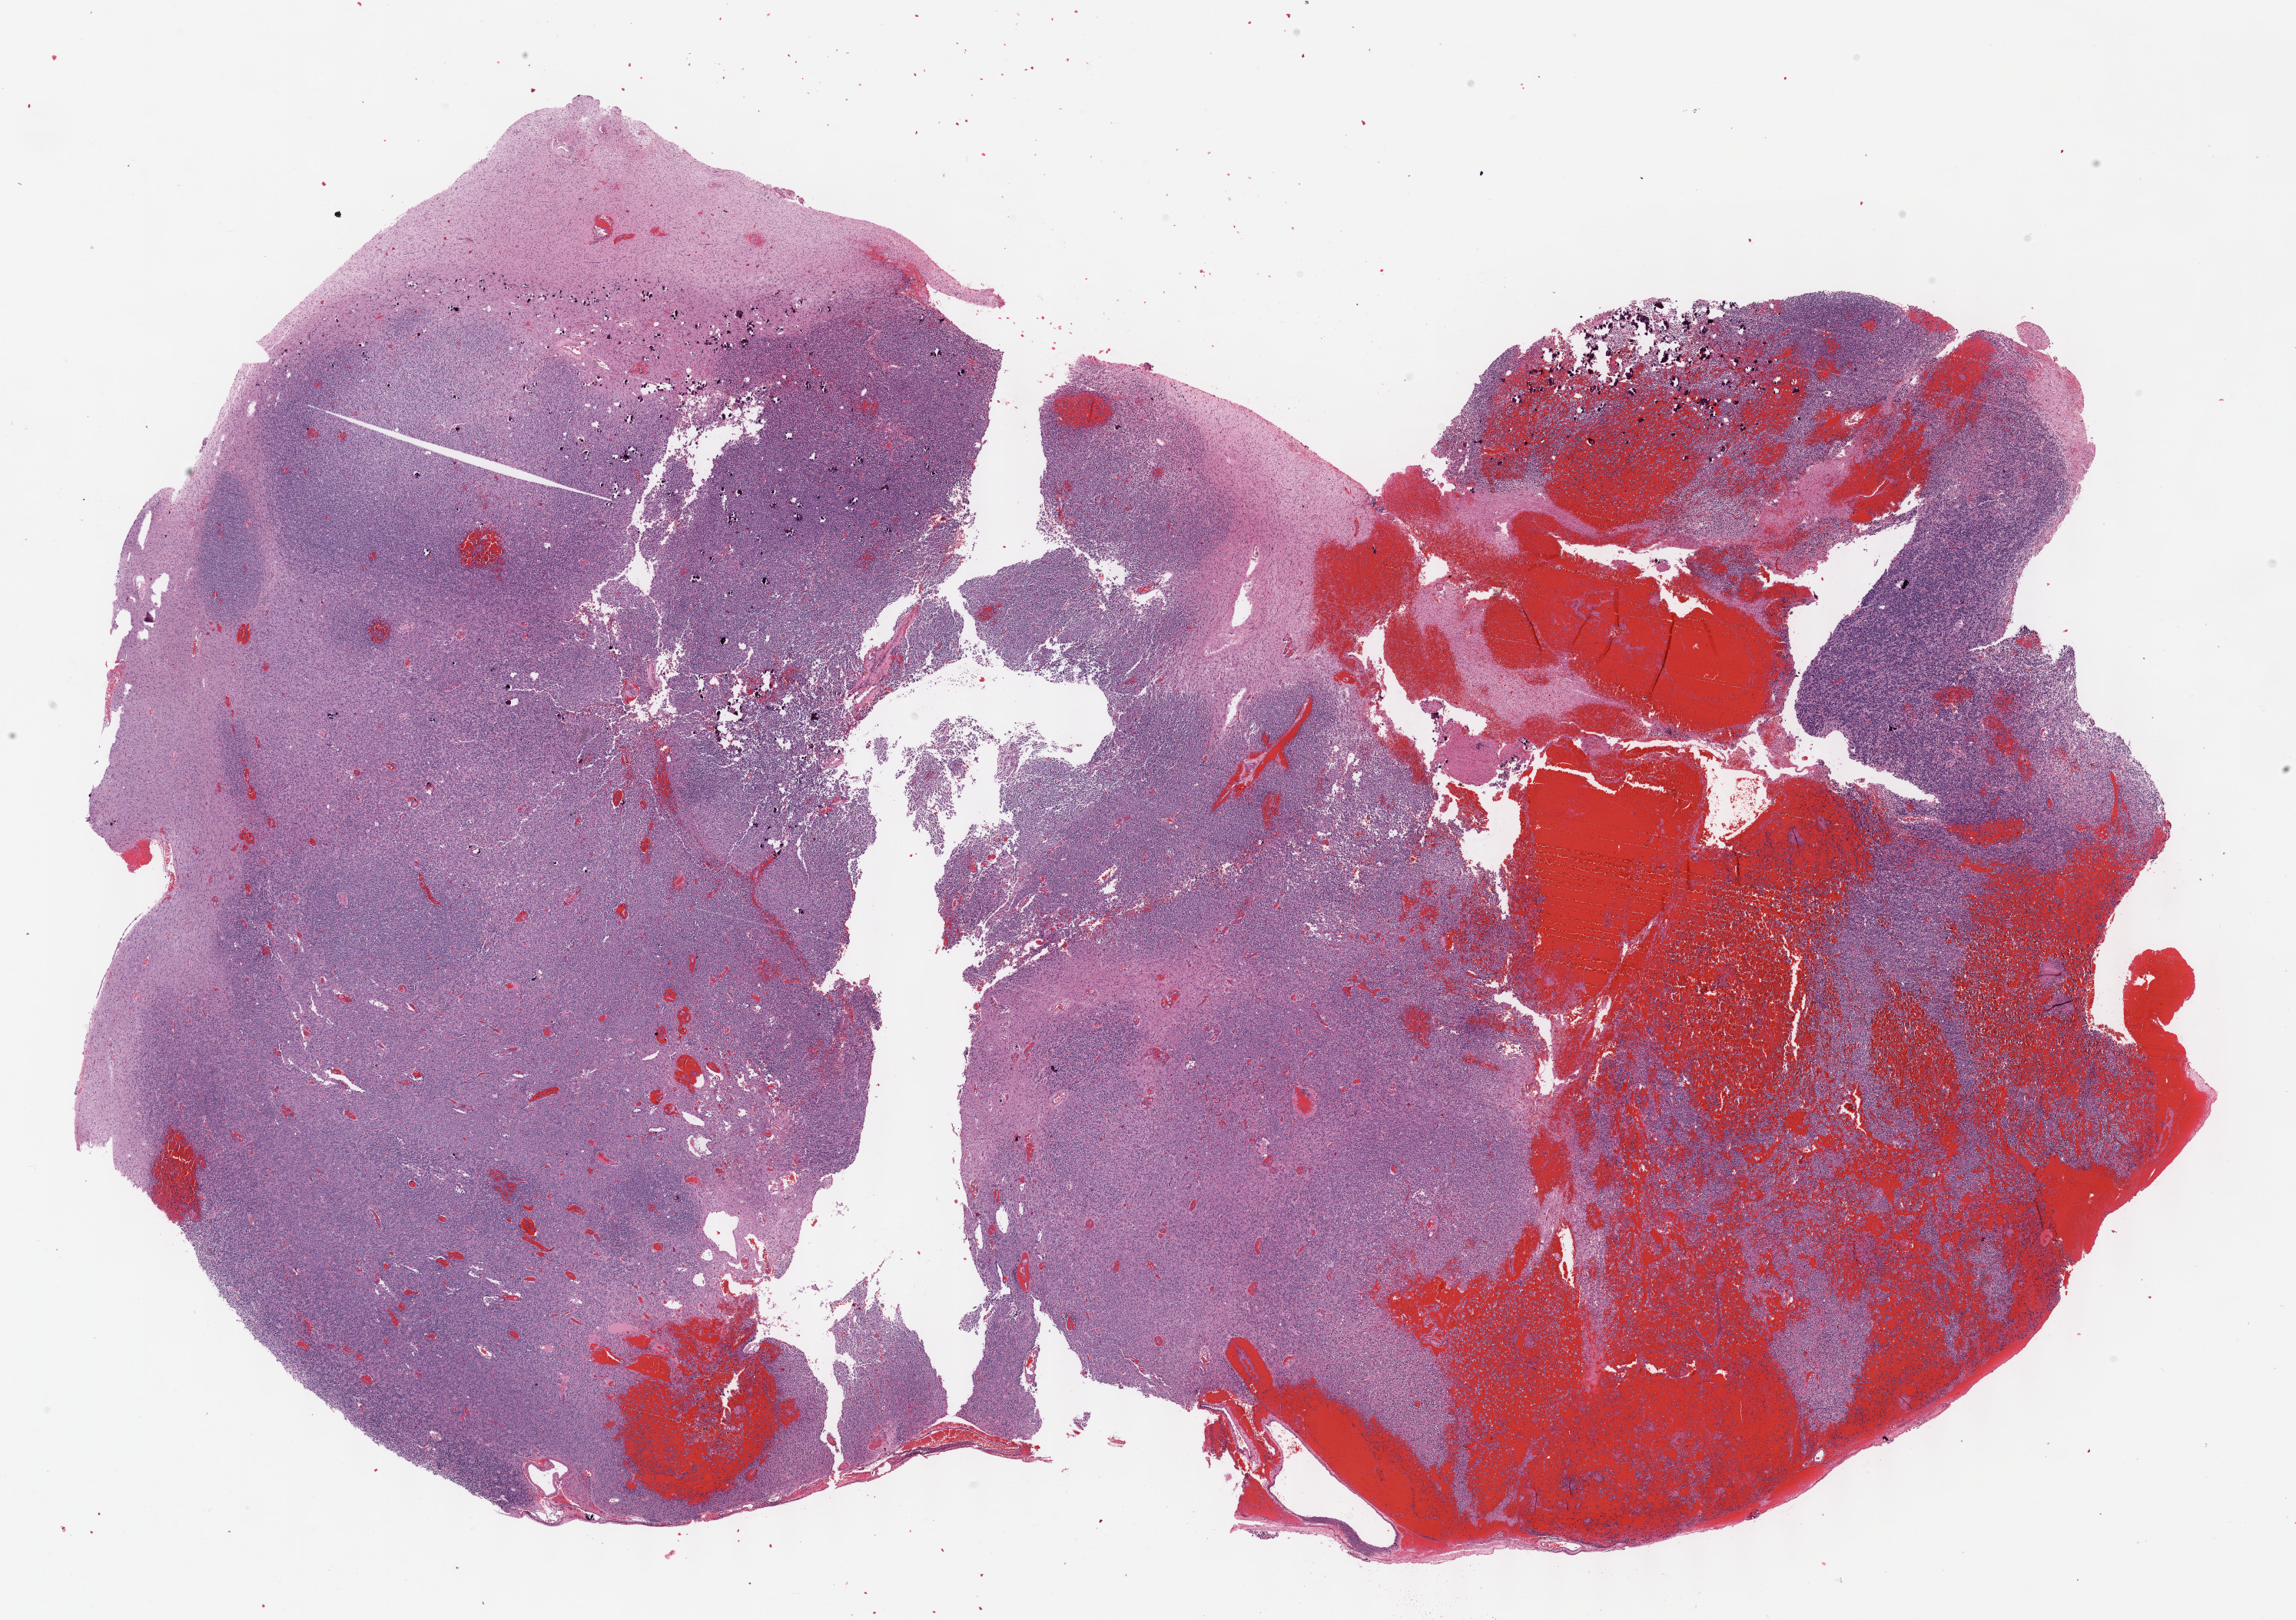
Whole-slide histology image, H&E — low-resolution overview of the scanned area, about 24.1 x 17.0 mm; formalin-fixed paraffin-embedded (FFPE) diagnostic section; brain, primary tumour sample. Male, age 54 years at initial diagnosis.
Diagnosis: Oligodendroglioma, anaplastic (cerebrum).